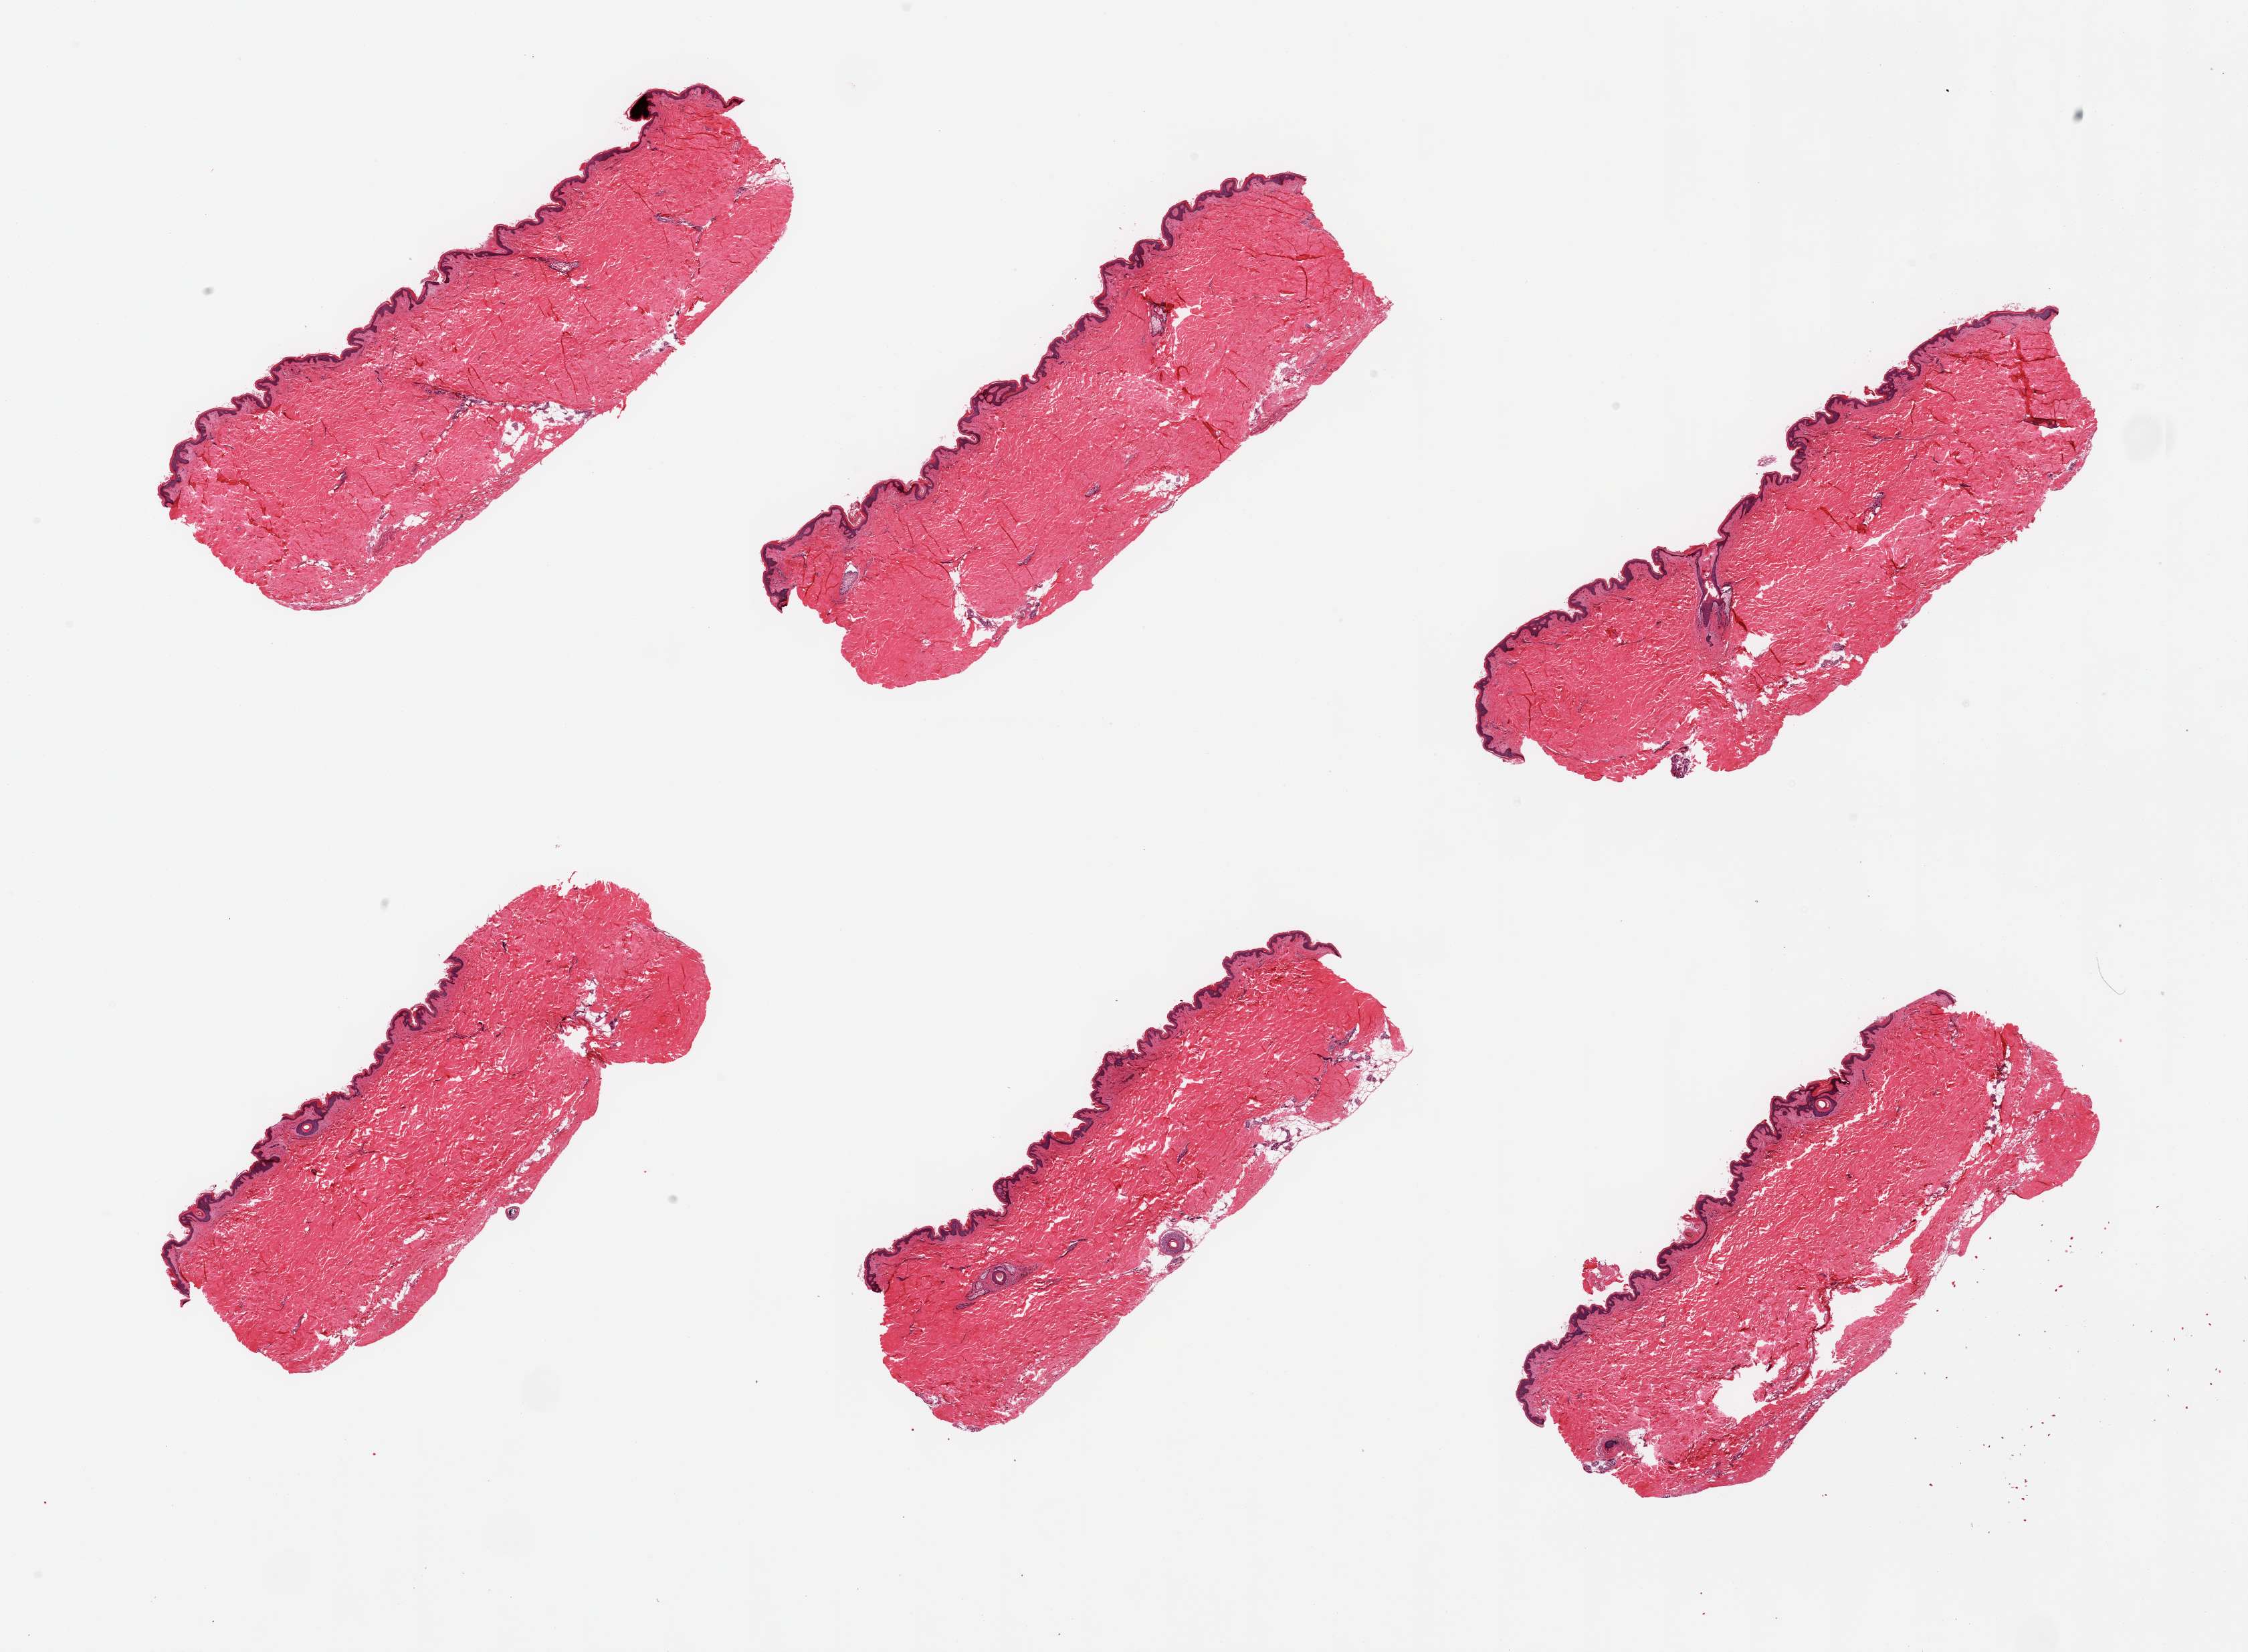
Digitized hematoxylin and eosin (H&E)-stained section, shown as a low-resolution overview of the whole scanned area (about 26.6 x 19.5 mm). PAXgene-fixed paraffin-embedded (PFPE) section. Section of skin of suprapubic region (target tissue). Tissue donor sample. Donor: male.
* pathologist's review note for this sample: 6 pieces, no adherent fat, squamous epithelium is ~30-40 microns